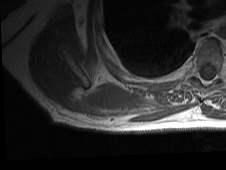
MRI of an extremity soft-tissue mass, one axial slice. Position 17 of 81 along the scan axis. MR volume resampled by the dataset authors to the PET/CT grid (not the native acquisition matrix). 3.27 mm slice thickness. 226 × 170 image matrix, field of view 221 × 166 mm. Male patient. Case-level facts recorded for this patient, not image findings: histological type: pleiomorphic spindle cell undifferentiated; grade: high; site of the primary tumour: right parascapusular.
Annotated regions visible in this slice (expert contour drawn on MRI and transferred to this co-registered scan by the dataset authors):
- gross tumour volume including surrounding oedema: bounding box (x1, y1, x2, y2) in pixels: (83, 86, 189, 123)